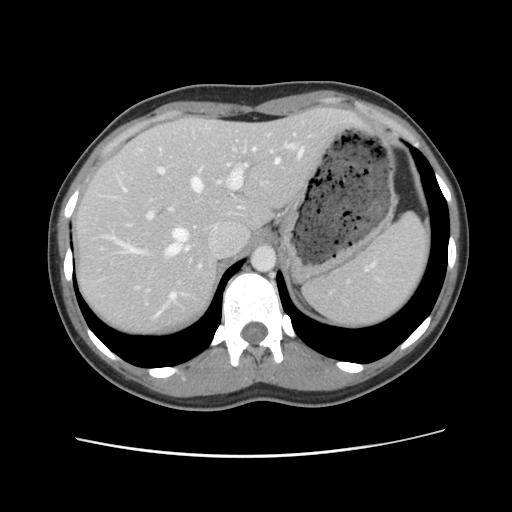
Contrast-enhanced abdominal CT, one axial slice. 120 kVp. Intravenous contrast given. Soft-tissue window (W 400 / L 40 HU). 2.5 mm slice thickness. 512 × 512 image matrix, field of view 339 × 339 mm. Female patient, age 33 years. Case-level facts recorded for this patient, not image findings: diagnosis: colorectal cancer liver metastases, imaged before liver resection.
Annotated regions visible in this slice (manually delineated by an expert):
- hepatic veins: bounding box (x1, y1, x2, y2) in pixels: (125, 148, 304, 300)
- liver: (73, 109, 358, 336)
- planned liver remnant (the part of the liver to remain after resection): (75, 109, 357, 336)
- portal vein (with intrahepatic branches): (147, 139, 295, 219)